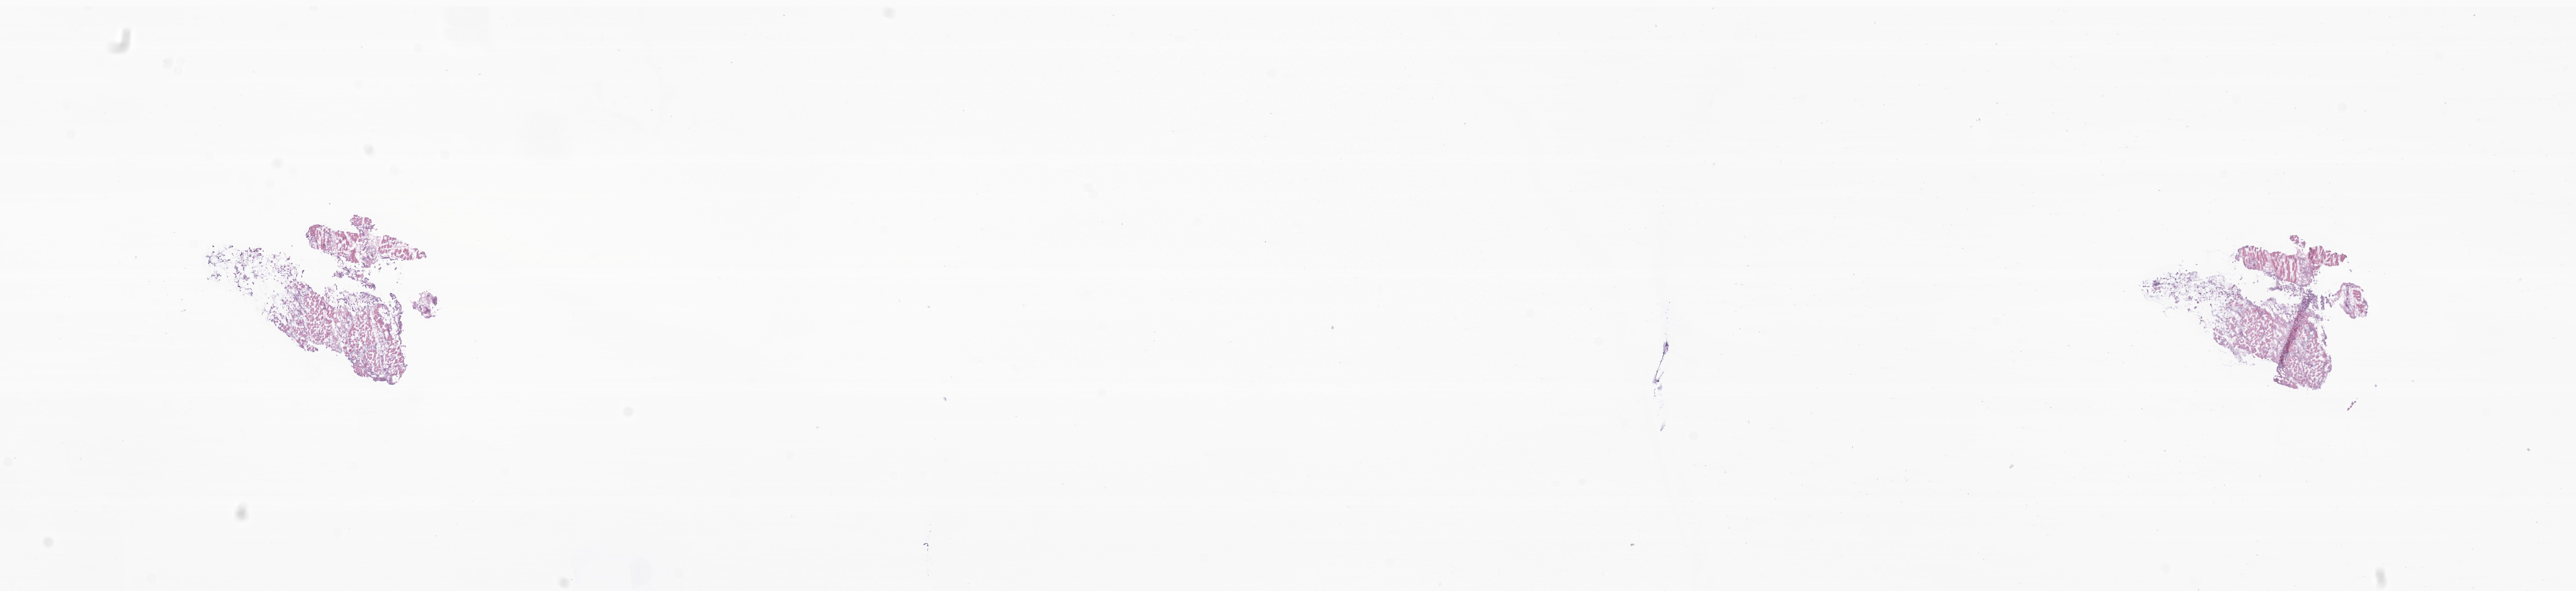
Whole-slide image, hematoxylin and eosin (H&E) stain of tumor tissue from the liver — a low-resolution overview of the entire scanned area, about 24.1 x 5.5 mm; frozen section (OCT-embedded). Patient male; age 176 days.
* recorded diagnosis: Atypical teratoid/rhabdoid tumor